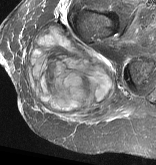
MRI of an extremity soft-tissue mass, one axial slice. Position 27 of 57 along the scan axis. STIR. MR volume resampled by the dataset authors to the PET/CT grid (not the native acquisition matrix). 3.27 mm slice thickness. 156 × 165 image matrix, field of view 152 × 161 mm. Female patient. From the clinical record (not read from this slice): histological type: epithelioid sarcoma with vascular differentiation; site of the primary tumour: right buttock.
Outlined on this slice (expert contour drawn on MRI and transferred to this co-registered scan by the dataset authors):
- gross tumour volume (mass): bounding box [x1, y1, x2, y2] px = [26, 28, 116, 120]